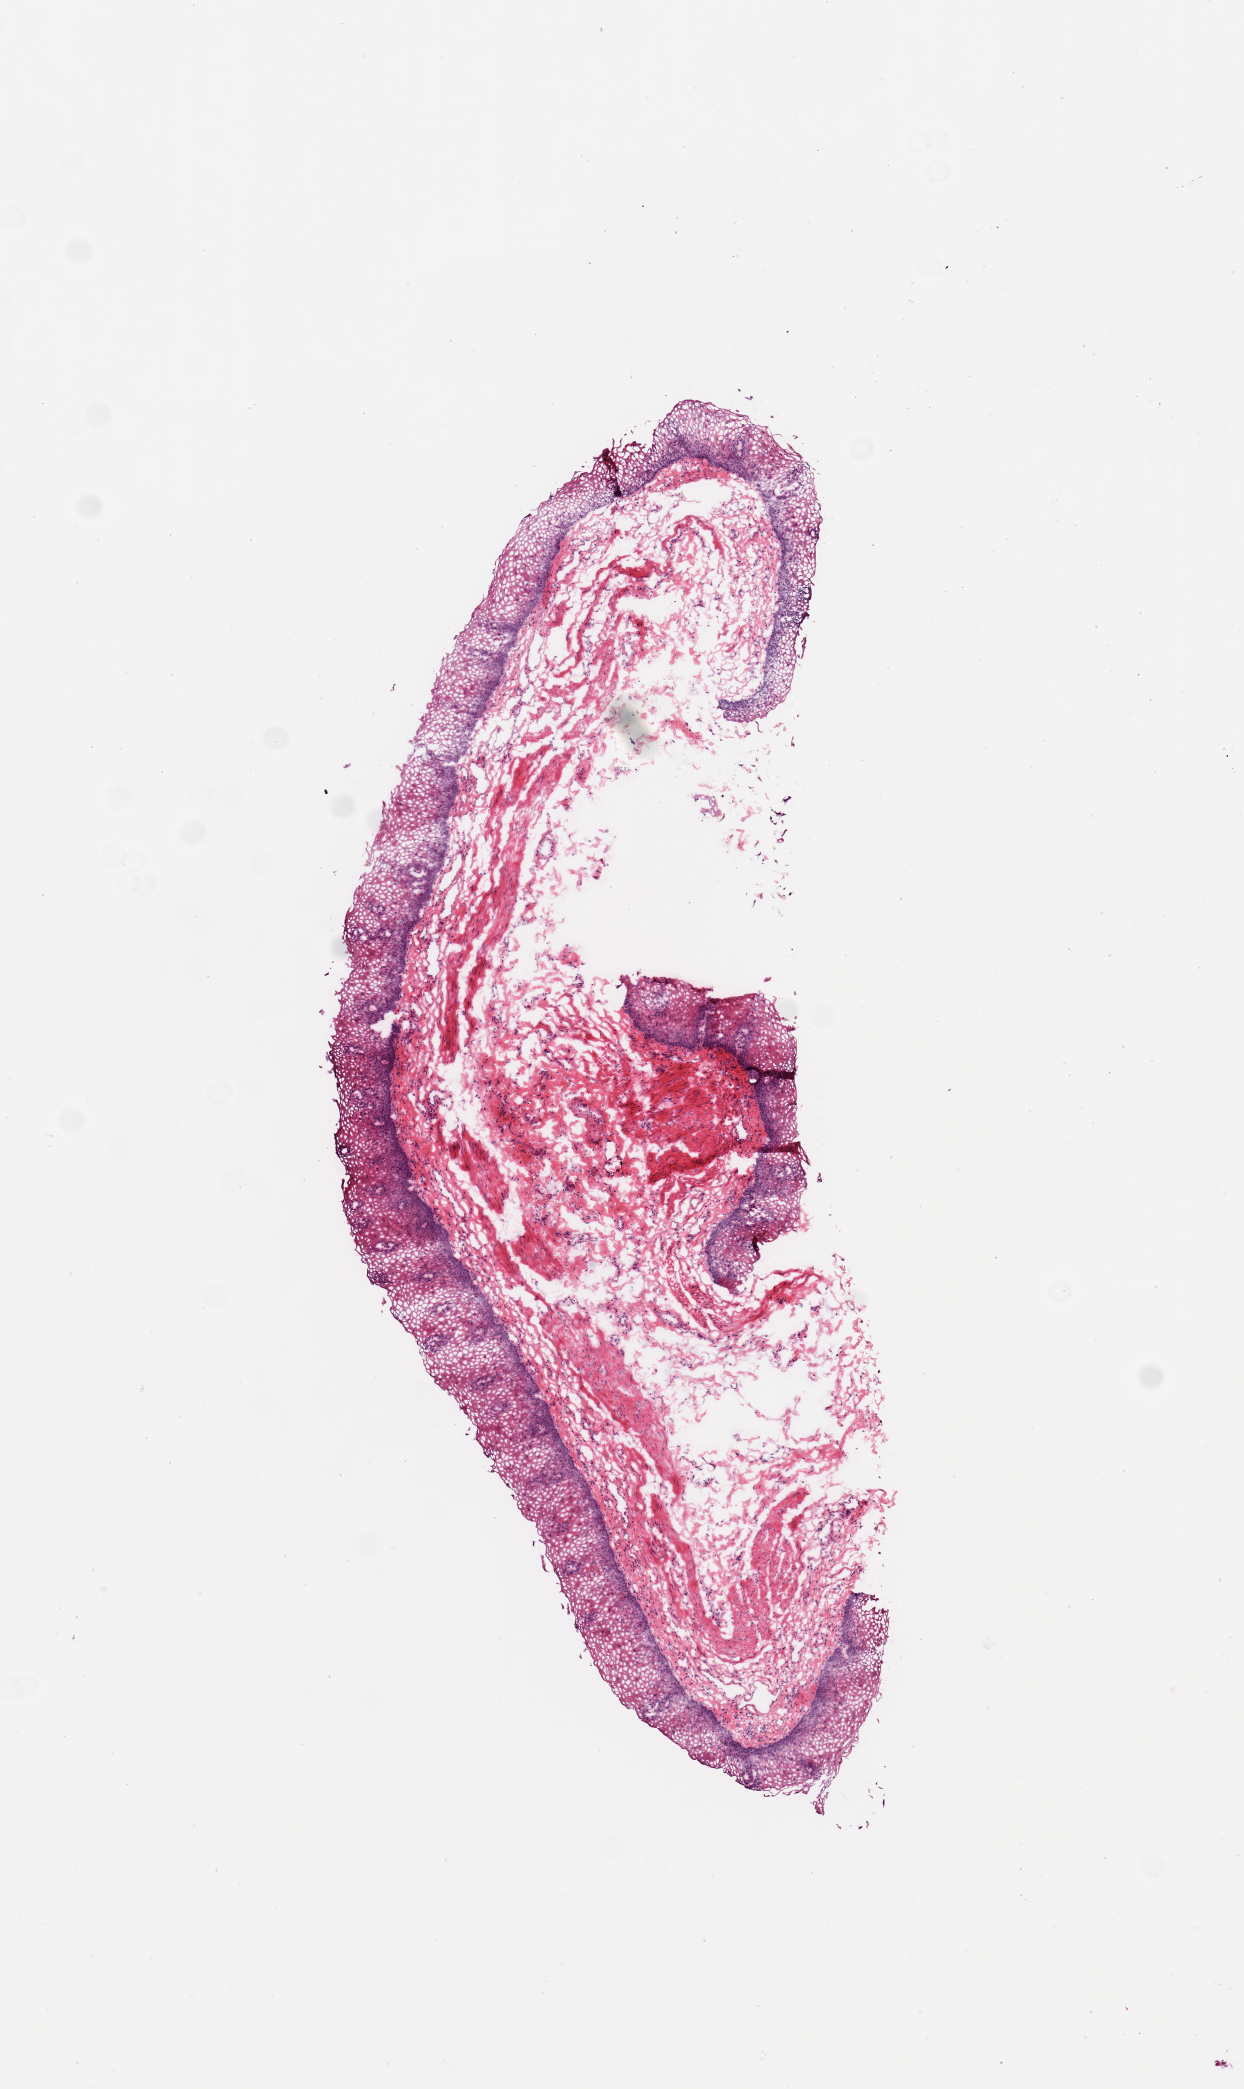
Whole-slide image, haematoxylin and eosin stain, brightfield — a low-resolution overview of the entire scanned area, about 4.9 x 8.3 mm (slide scanned at 20x). Frozen section. Sampled site (target tissue): esophageal mucous membrane. Tissue donor sample. Donor sex: female.
Reviewer comment on this tissue sample: 1 piece.